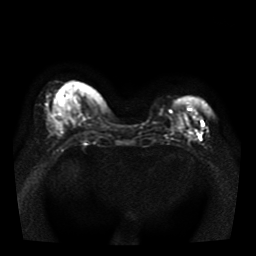
Breast MRI, one axial slice. Slice 15 of 41 in the series (ordered by position). Diffusion-weighted series; image 2 of 4 stored at this slice position (different b-values; order by instance number). 1.5 T. 5 mm slice thickness. 256 × 256 image matrix. Female patient.
Structures marked on this image (expert manual segmentation):
- tumour on diffusion-weighted imaging: box from (x=187, y=128) to (x=193, y=135) px